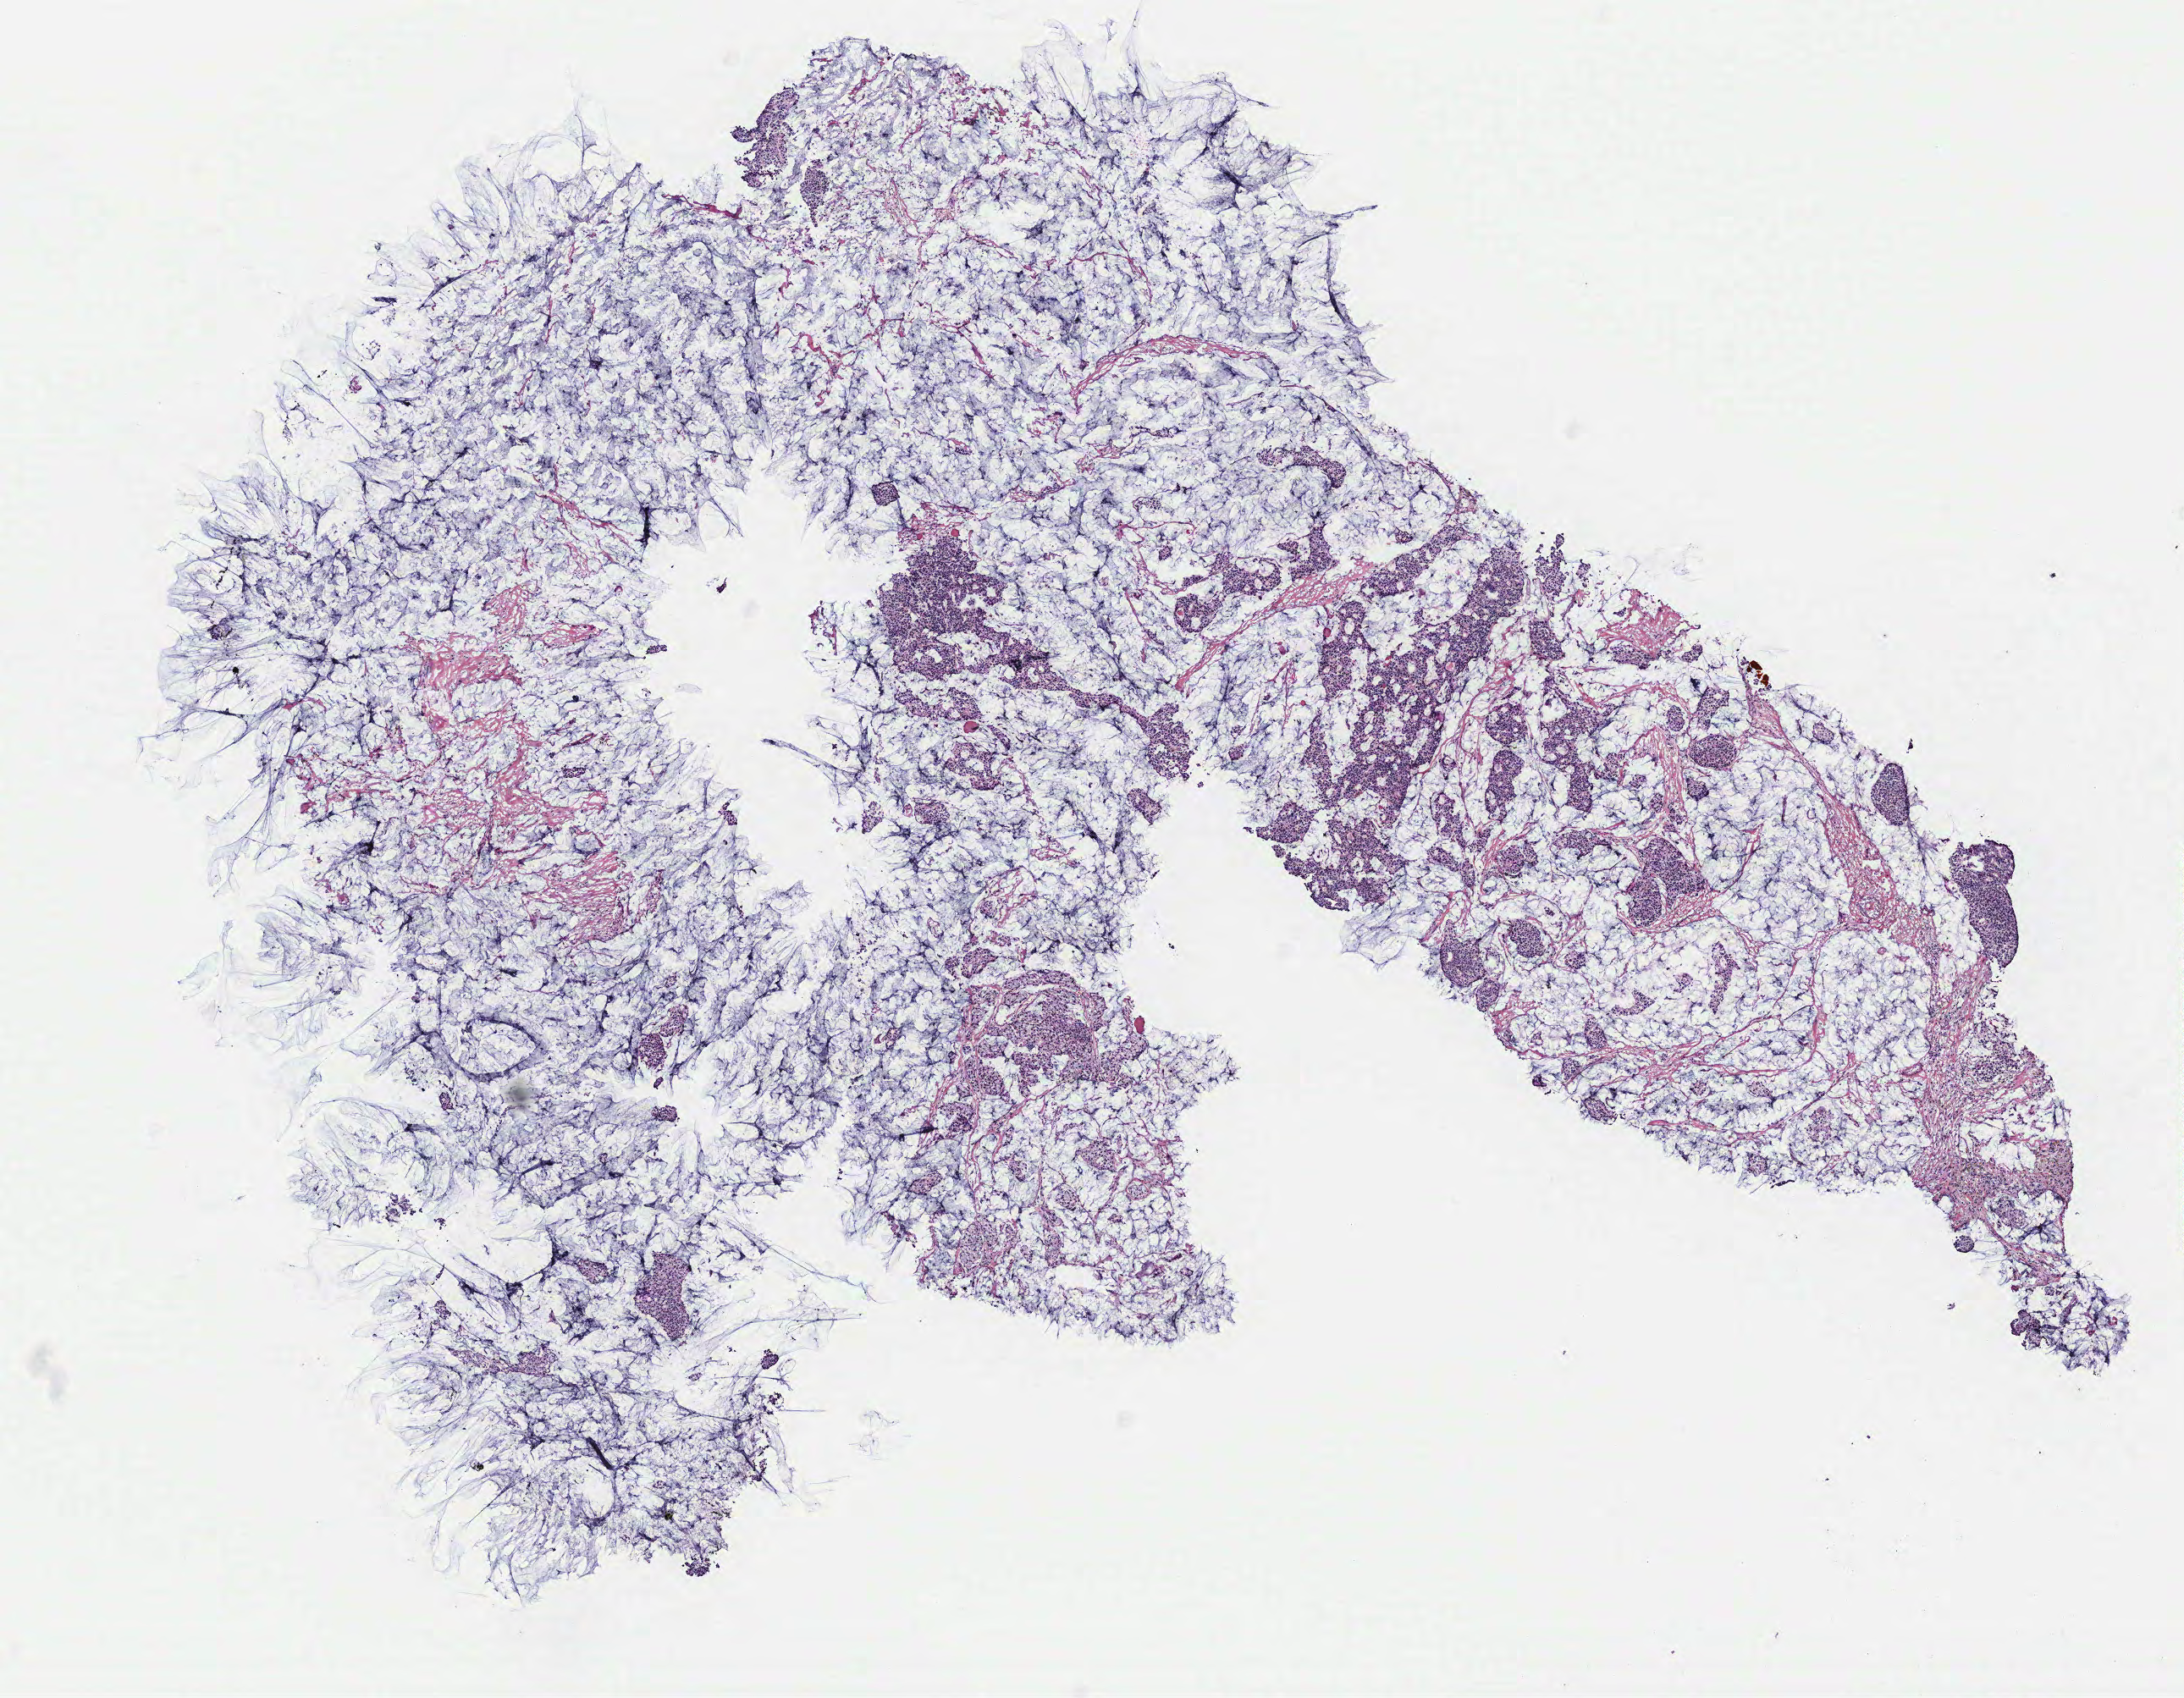
Whole-slide histology image, H&E — a low-resolution overview of the entire scanned area, about 10.3 x 8.0 mm. Breast, tissue type not recorded. Female, 81 y/o.
Patient diagnosis: Infiltrating duct carcinoma, NOS.